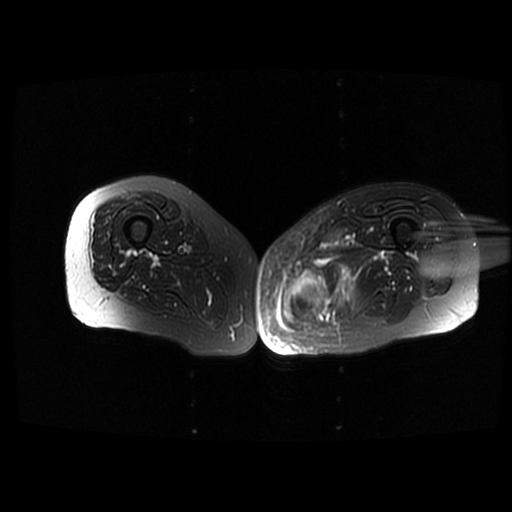
MRI of an extremity soft-tissue mass, one axial slice; position 40 of 42 along the scan axis; T2-weighted fat-saturated; 6 mm slice thickness; 512 × 512 image matrix, field of view 420 × 420 mm. Female patient. From the clinical record (not read from this slice): histological type: pleomorphic leiomyosarcoma; grade: high; site of the primary tumour: left thigh.
Structures marked on this image (expert manual segmentation):
- gross tumour volume including surrounding oedema: bounding box [x1, y1, x2, y2] px = [284, 264, 354, 324]